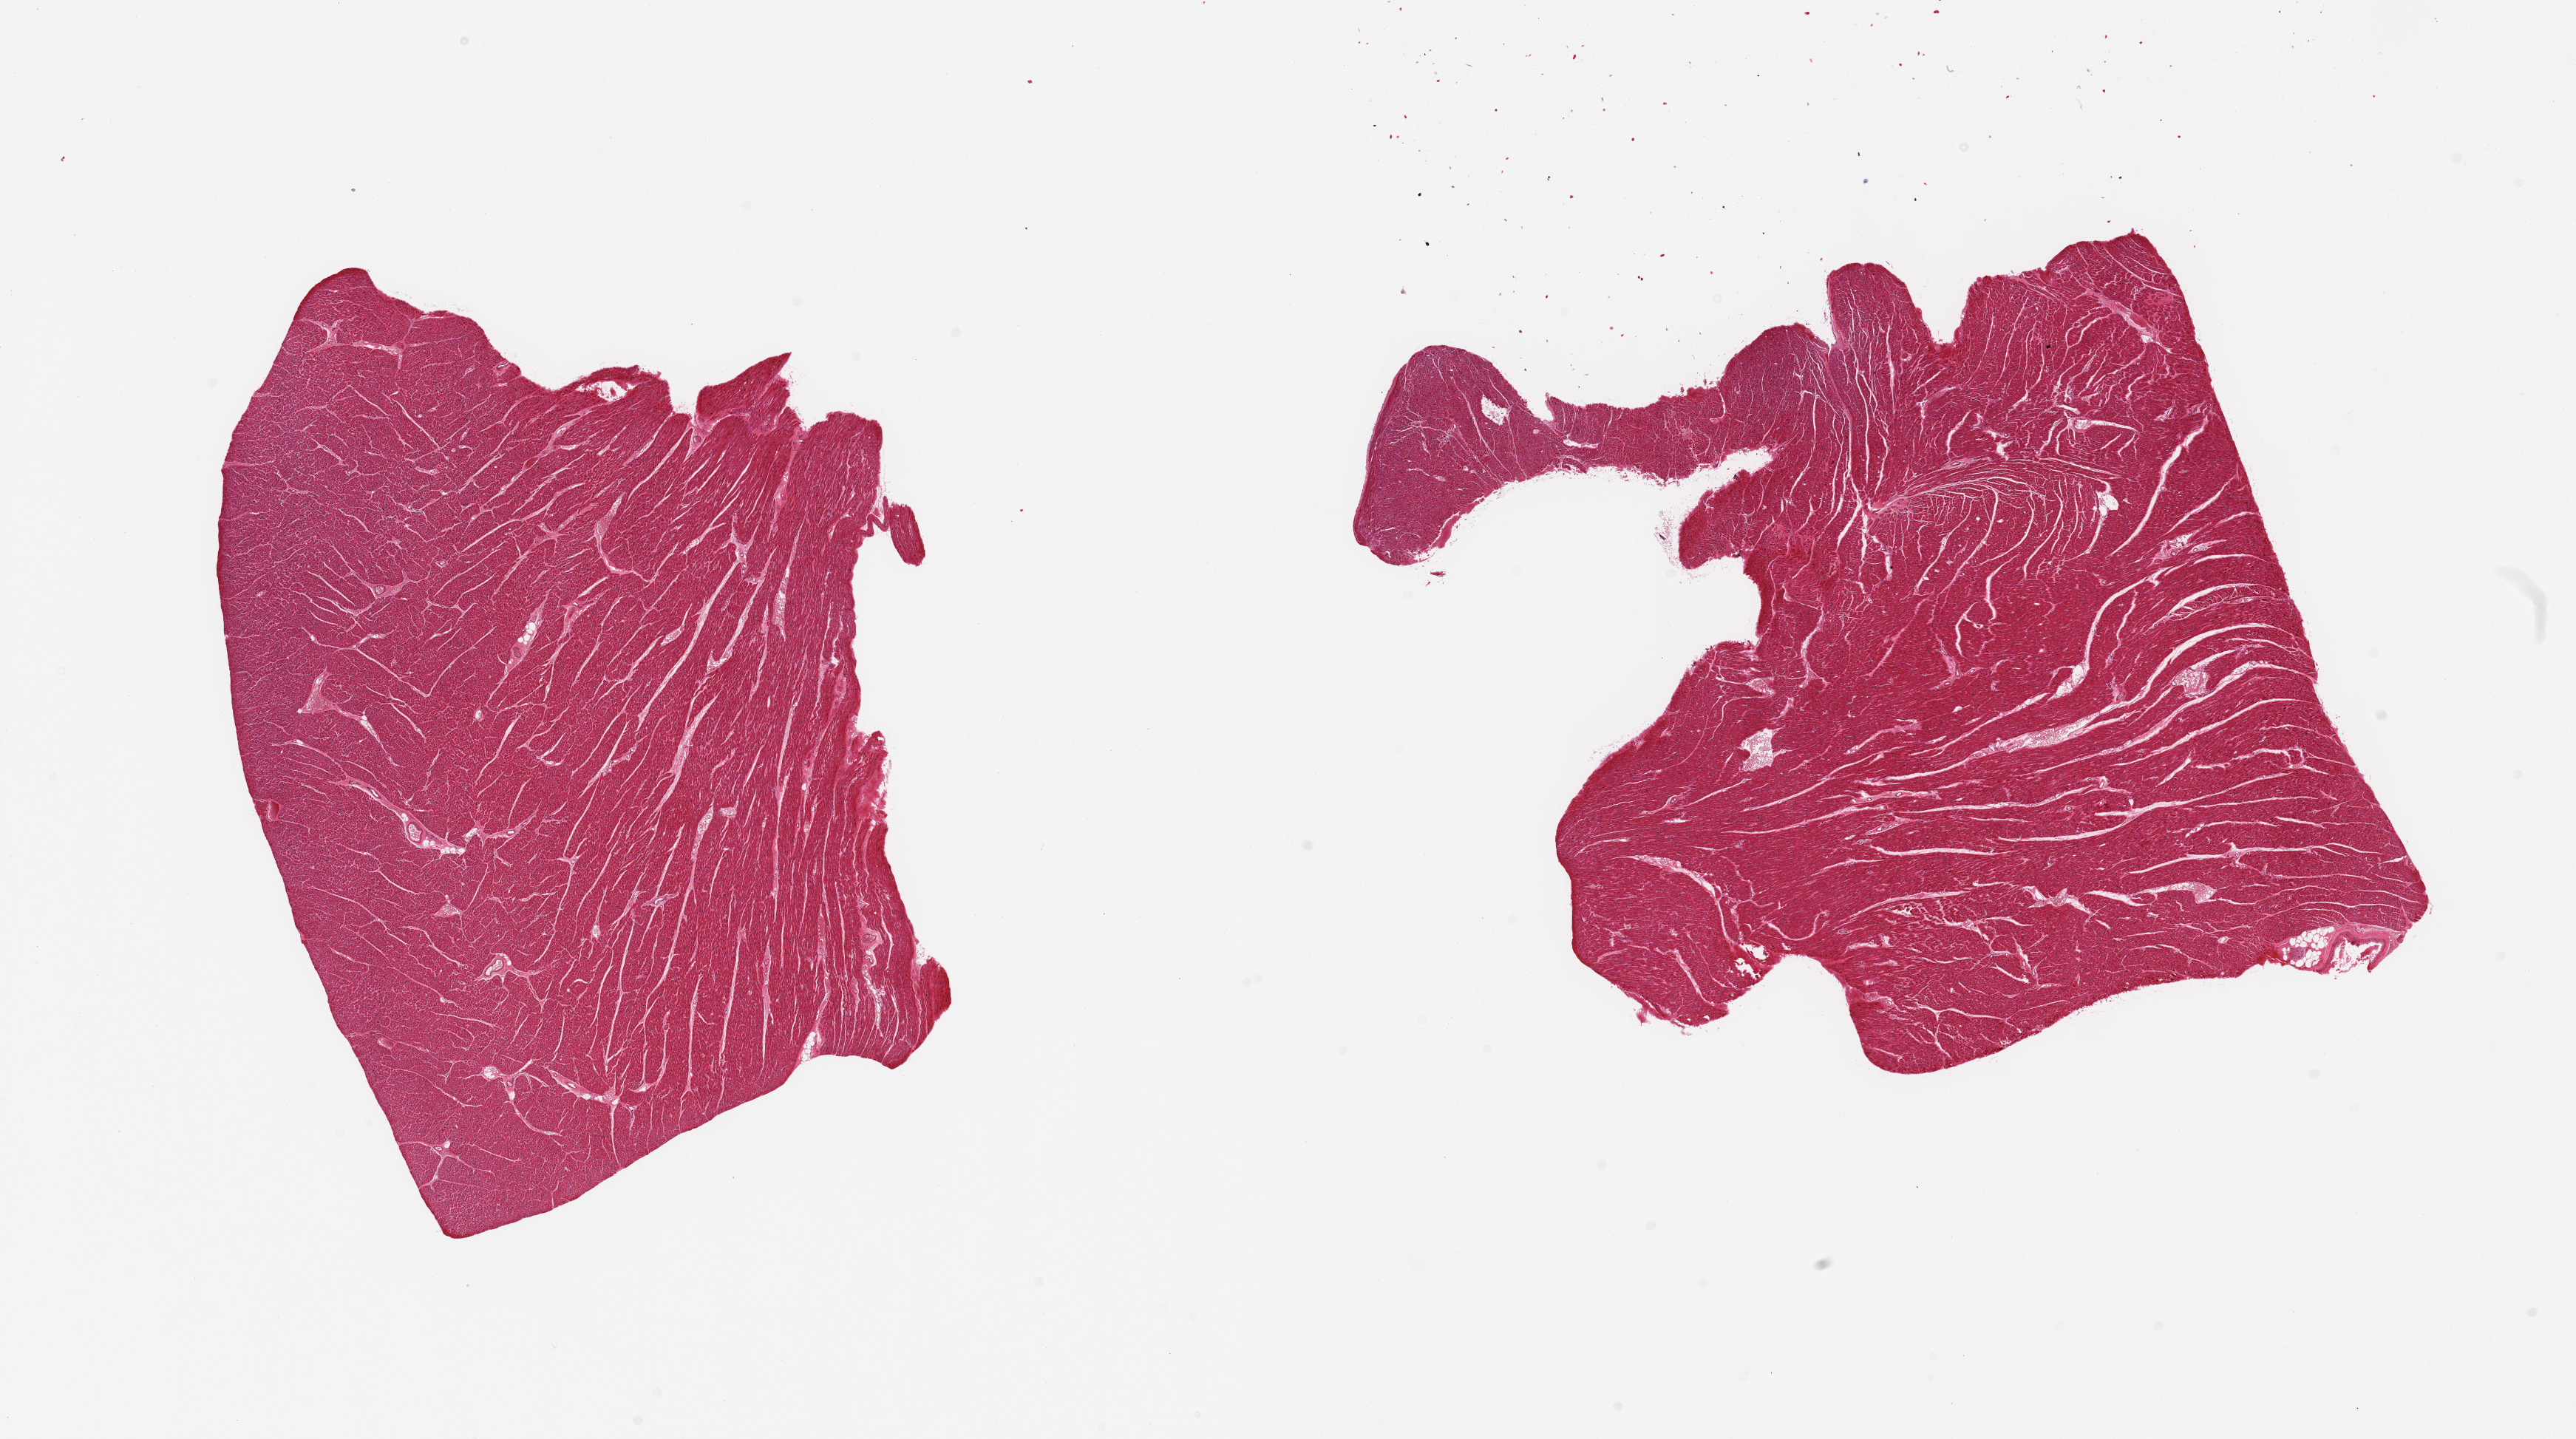
Whole-slide image, haematoxylin and eosin stain, brightfield — a low-resolution overview of the entire scanned area, about 27.6 x 15.4 mm (from a 20x scan). PAXgene-fixed, paraffin-embedded tissue. Sampled site (target tissue): heart. Donor tissue sample. Donor sex: male.
Pathologist's review note for this sample: 2 pieces.